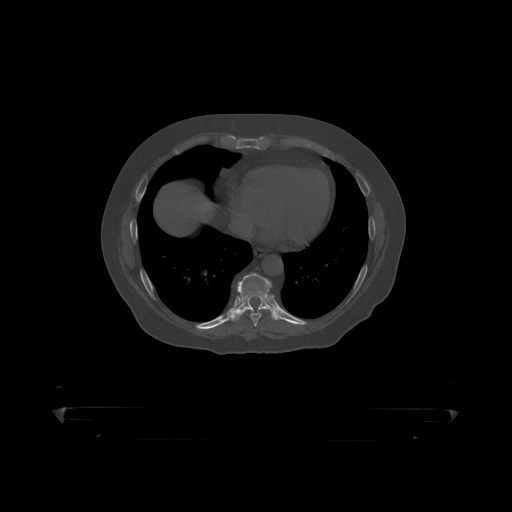
CT including the spine, one axial slice; slice 245 of 390 in the series (ordered by position); 120 kVp; bone window (W 1800 / L 400 HU); 1.25 mm slice thickness; 512 × 512 image matrix, field of view 650 × 650 mm. Male patient, age 60 years. Case-level facts recorded for this patient, not image findings: primary cancer: prostate.
Outlined on this slice (semi-automatically segmented with operator editing):
- T8 vertebra: bounding box [x1, y1, x2, y2] px = [250, 309, 263, 319]
- T9 vertebra: [233, 274, 274, 317]